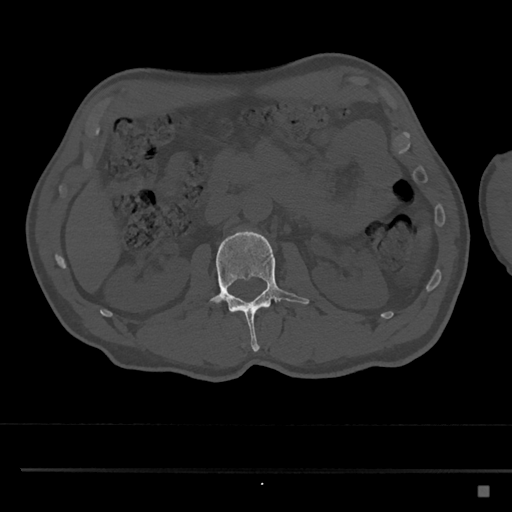
CT including the spine, one axial slice. Slice 759 of 797 in the series (ordered by position). 120 kVp. Bone window (W 1800 / L 400 HU). 512 × 512 image matrix, field of view 391 × 391 mm. Male patient, age 59 years. Case-level facts recorded for this patient, not image findings: primary cancer: prostate.
Structures marked on this image (semi-automatically segmented with operator editing):
- L2 vertebra: box from (x=211, y=230) to (x=309, y=352) px